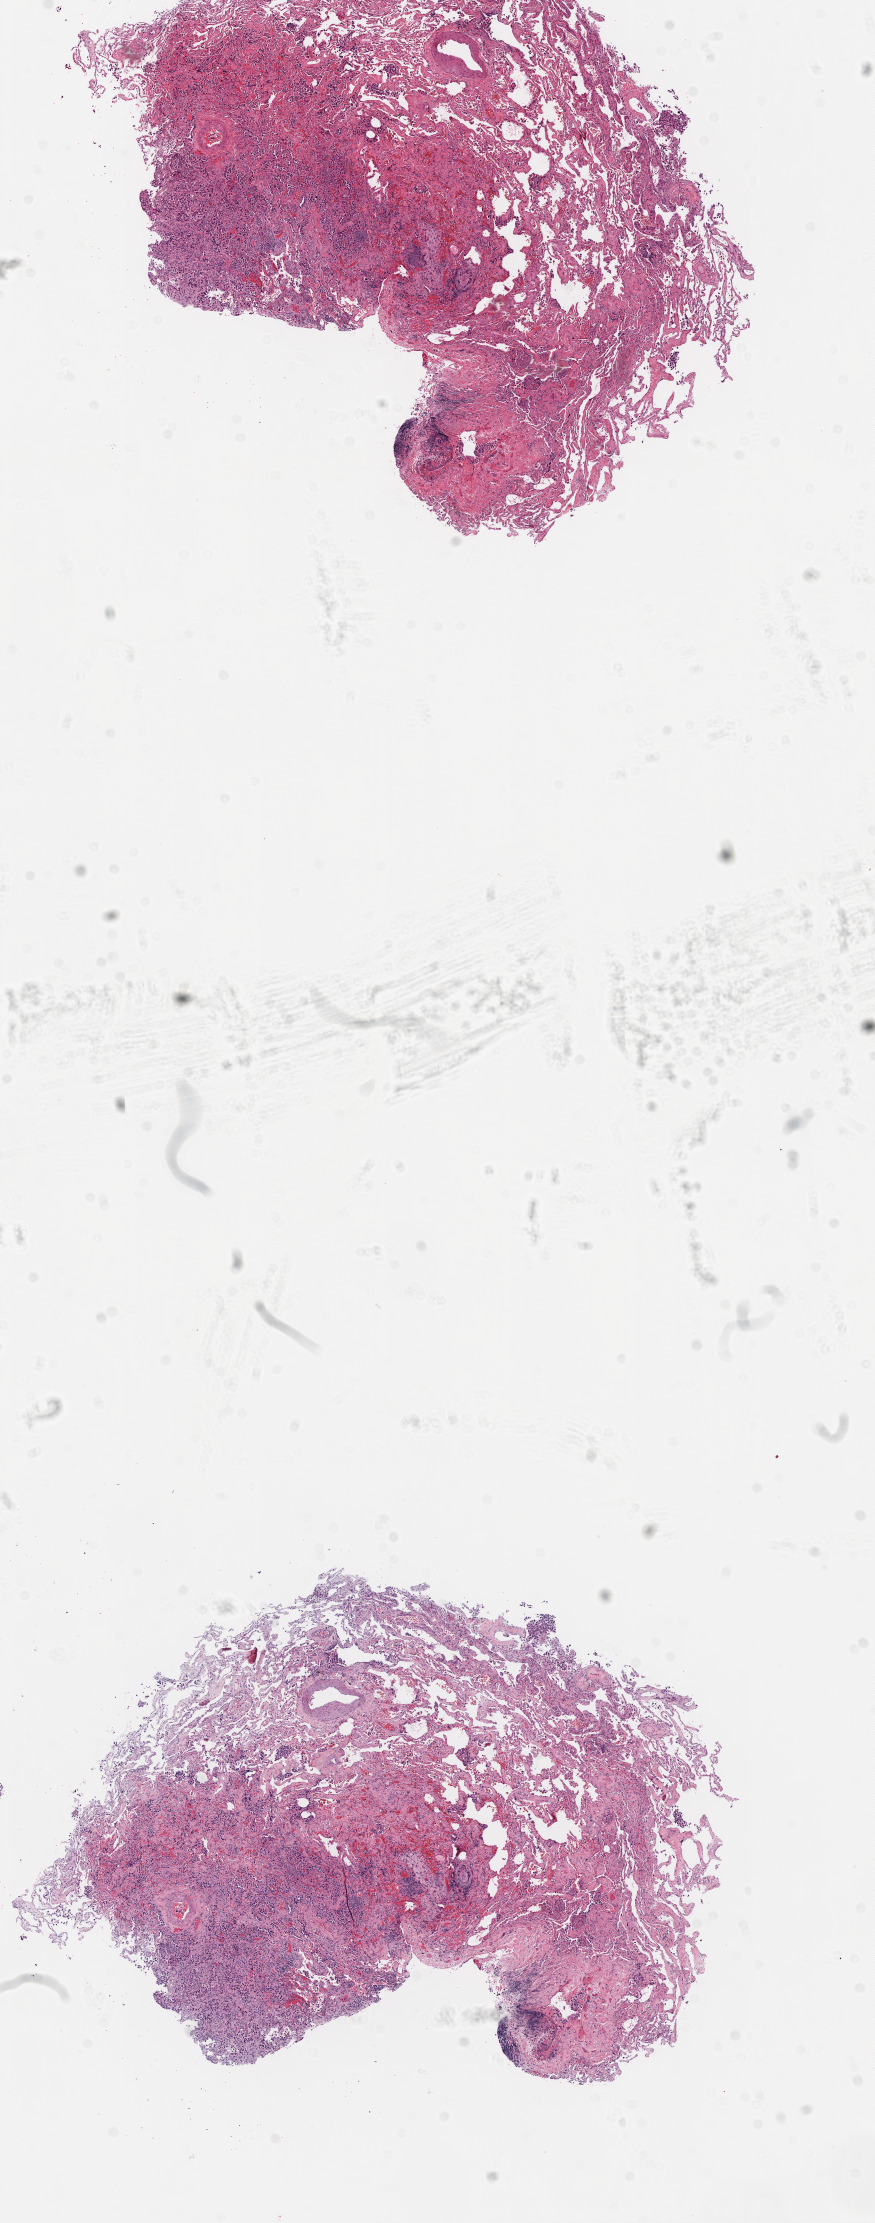
Whole-slide histology image, H&E-stained — whole scanned area (about 7.0 x 17.8 mm, acquisition: 20x scan) shown as a low-resolution overview, frozen section from the top of the tissue portion, sample: primary tumour, lung. Female patient; age at initial diagnosis 65 years. Slide review estimates, as recorded: tumour cells 35%, tumour nuclei 55%, normal cells 55%, stromal cells 10%, necrosis 0%. Infiltration values recorded for this section: lymphocyte infiltration 3%.
AJCC pathologic stage: IIB (6th edition). Histologic diagnosis: Adenocarcinoma, NOS. TNM: T1 N1 M0.